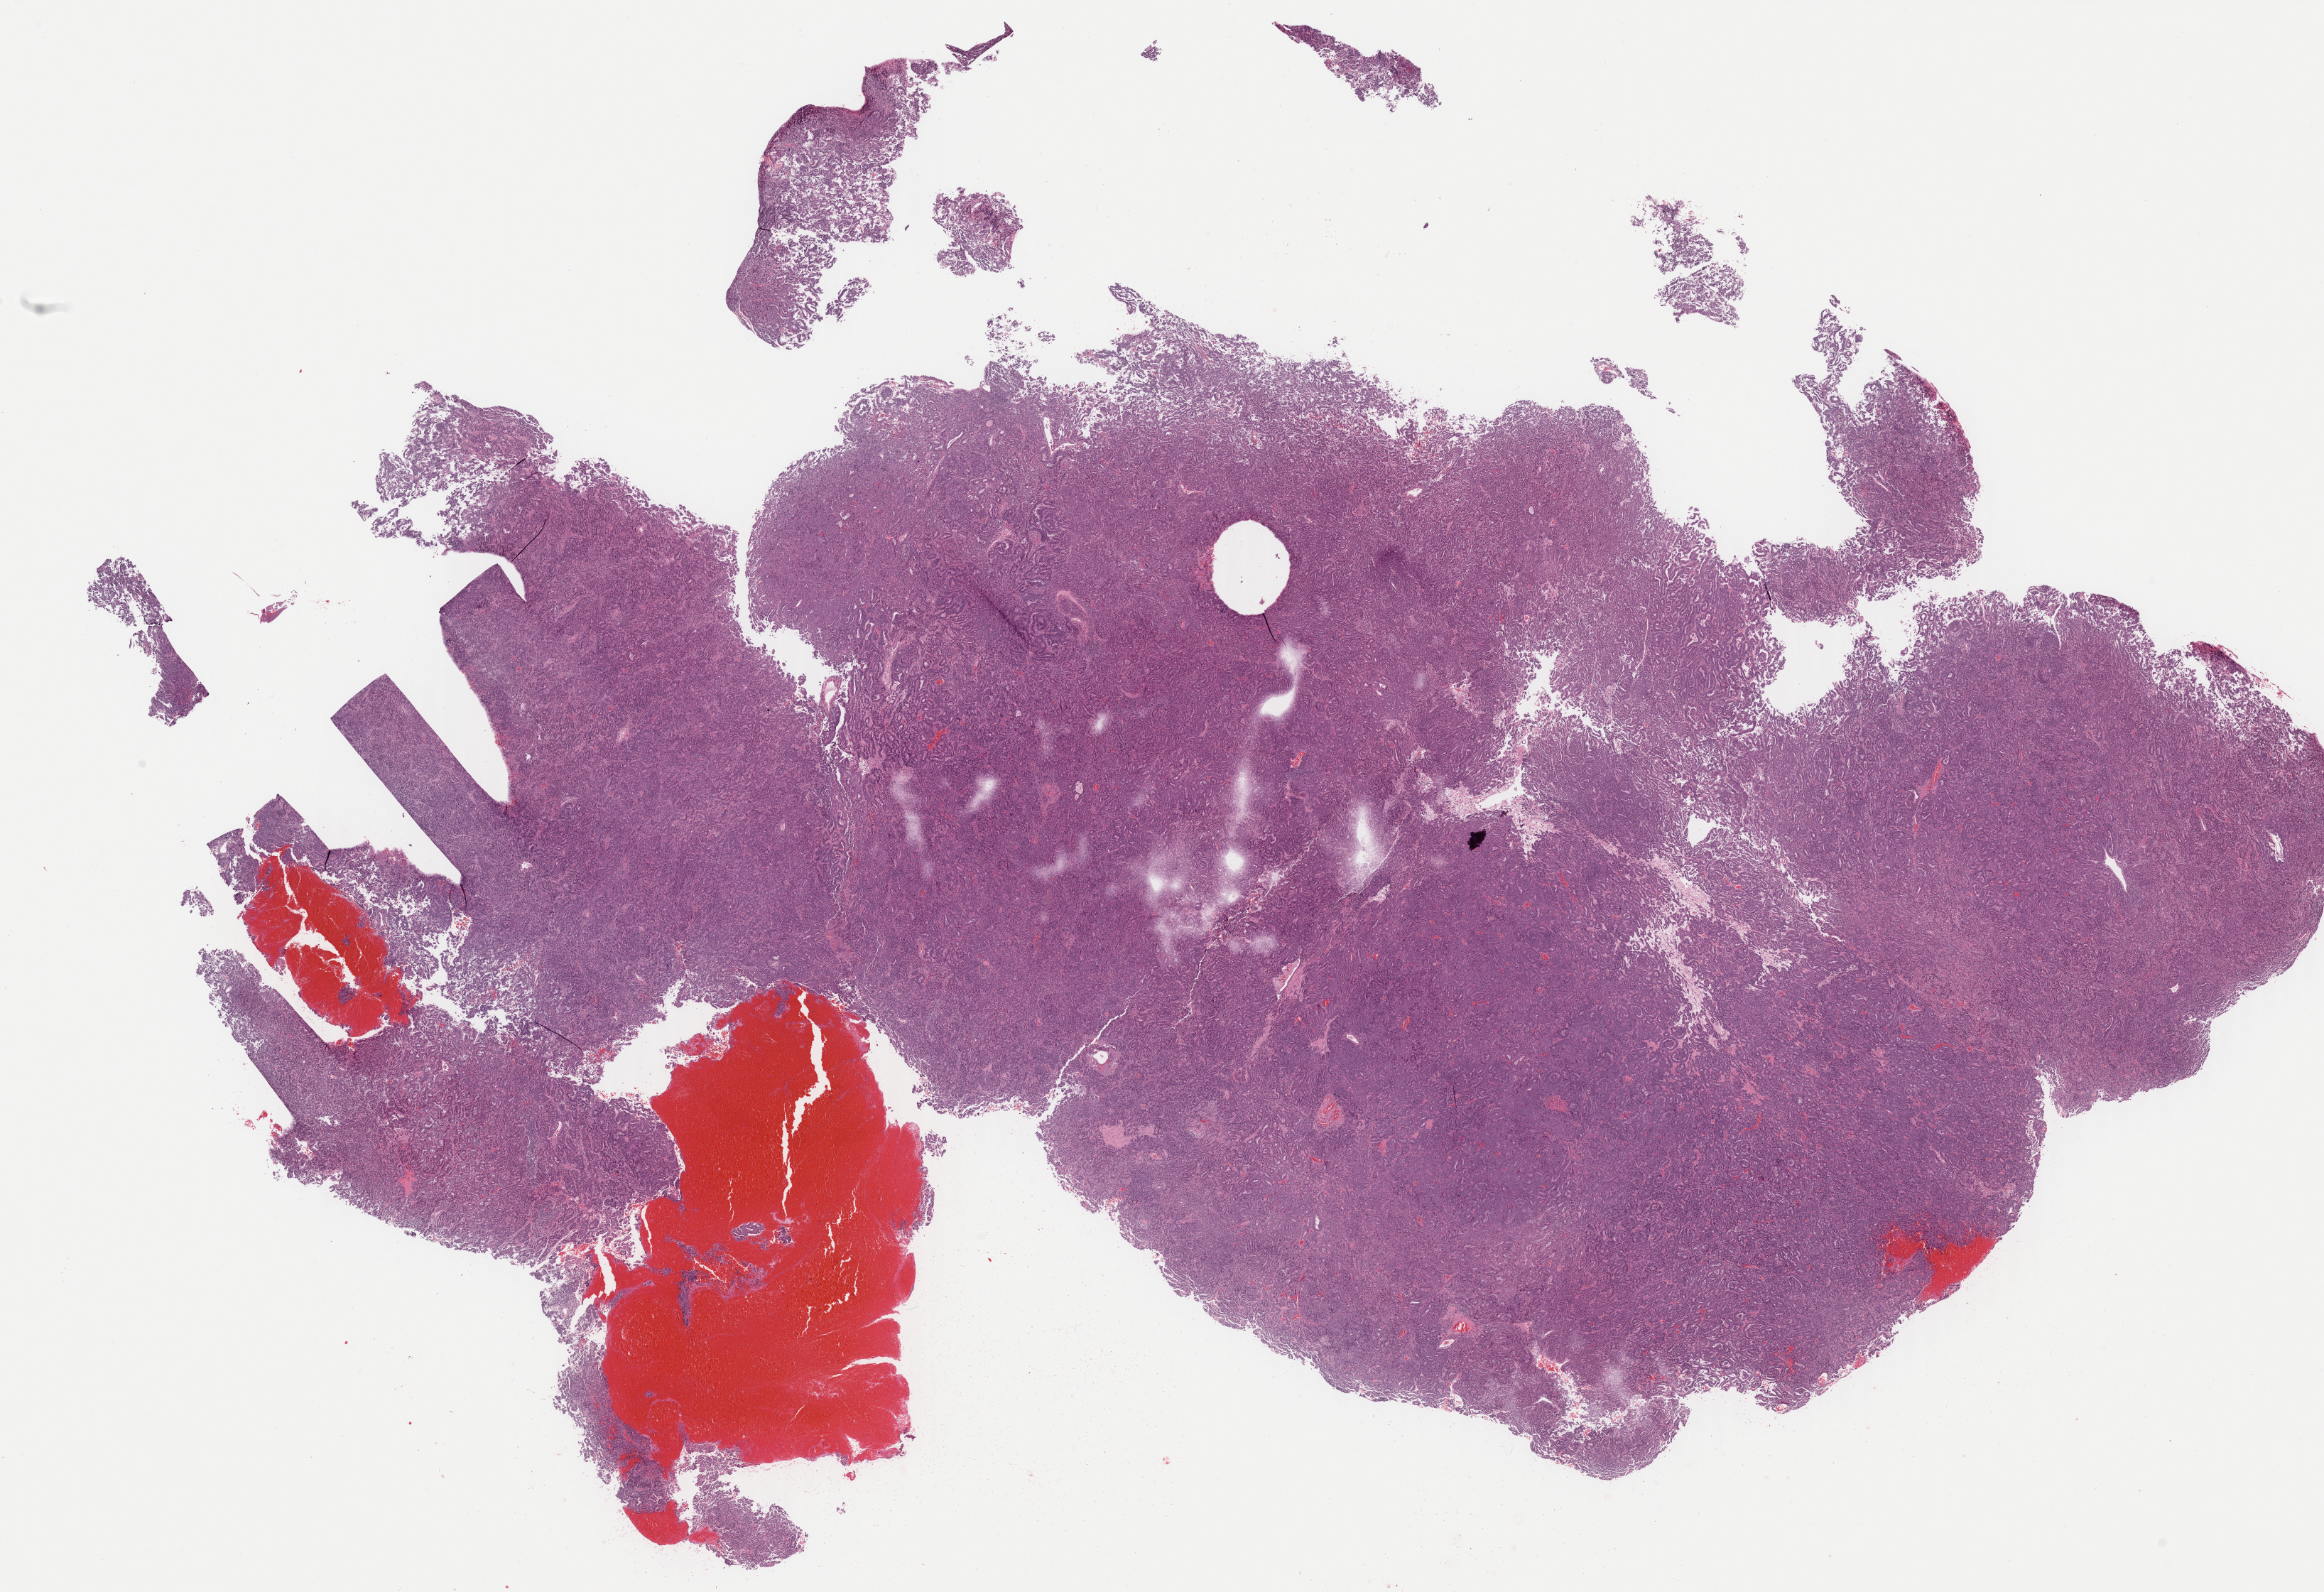
Whole-slide histology image, H&E-stained — shown as a low-resolution overview of the whole scanned area (about 25.9 x 17.7 mm), formalin-fixed paraffin-embedded (FFPE) diagnostic section, primary tumour sample from the uterus. Female patient; age at initial diagnosis 82 years. Histologic grade: G3 (poorly differentiated).
Pathologic diagnosis: Serous cystadenocarcinoma, NOS (endometrium). FIGO stage: IIIC2.